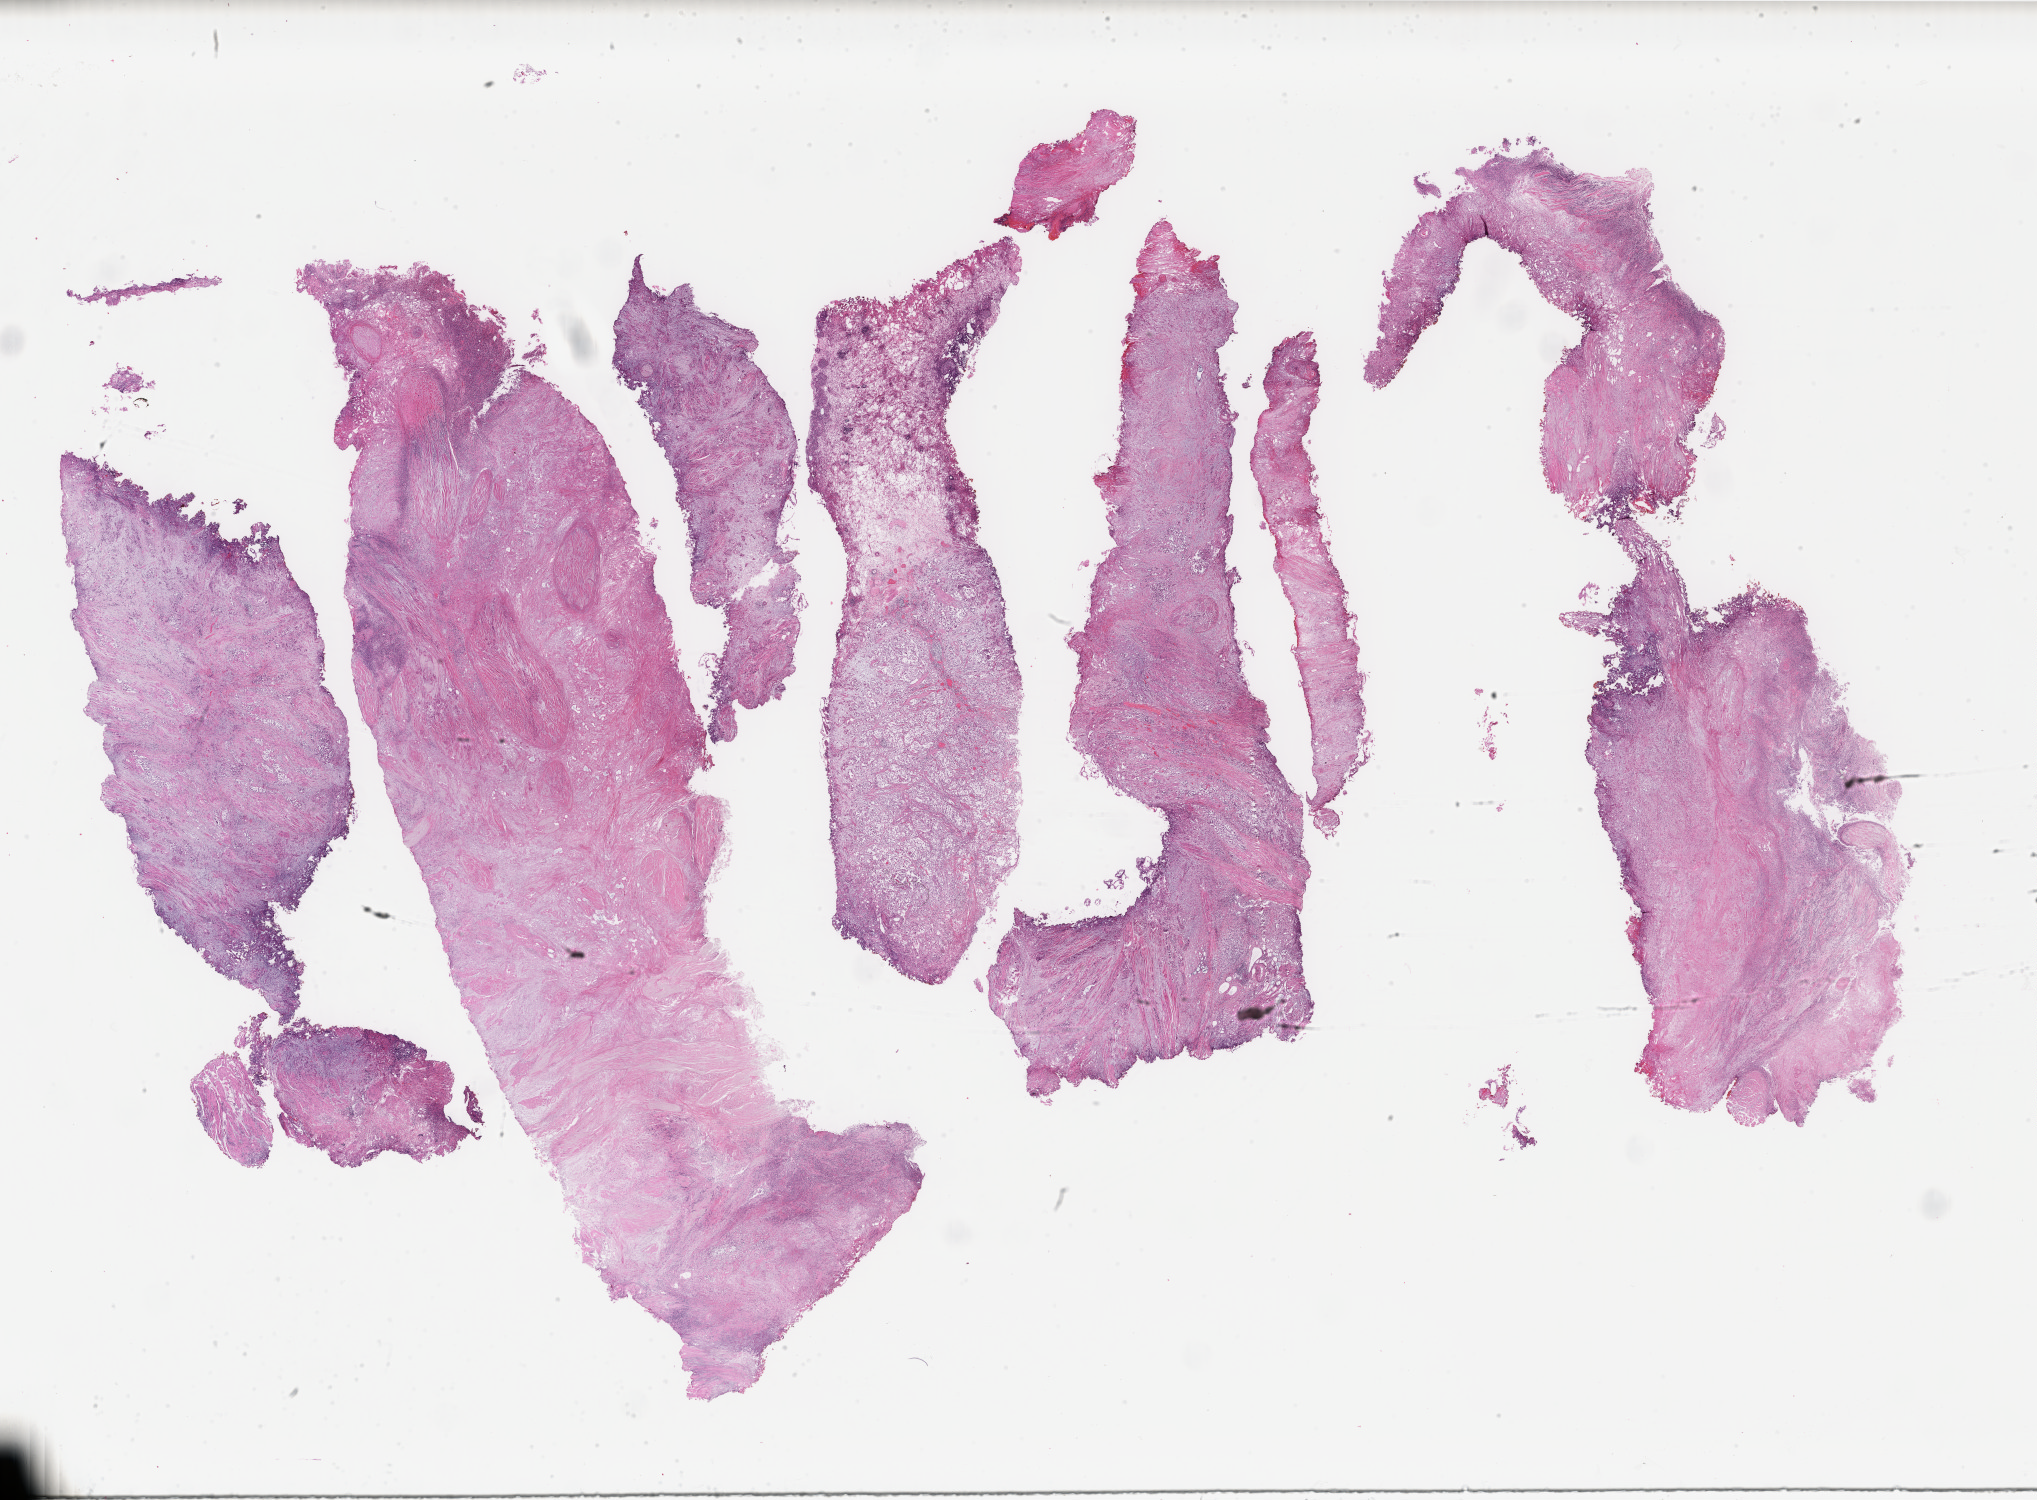
Hematoxylin and eosin (H&E) stained whole-slide image, low-resolution overview of the scanned area, about 32.3 x 23.8 mm; formalin-fixed paraffin-embedded (FFPE) diagnostic section; sample: primary tumour, bladder. Female, age 58 years at initial diagnosis. Histologic grade: high grade.
* AJCC pathologic stage: II (2nd edition)
* TNM: N0 M0
* histologic diagnosis: Transitional cell carcinoma